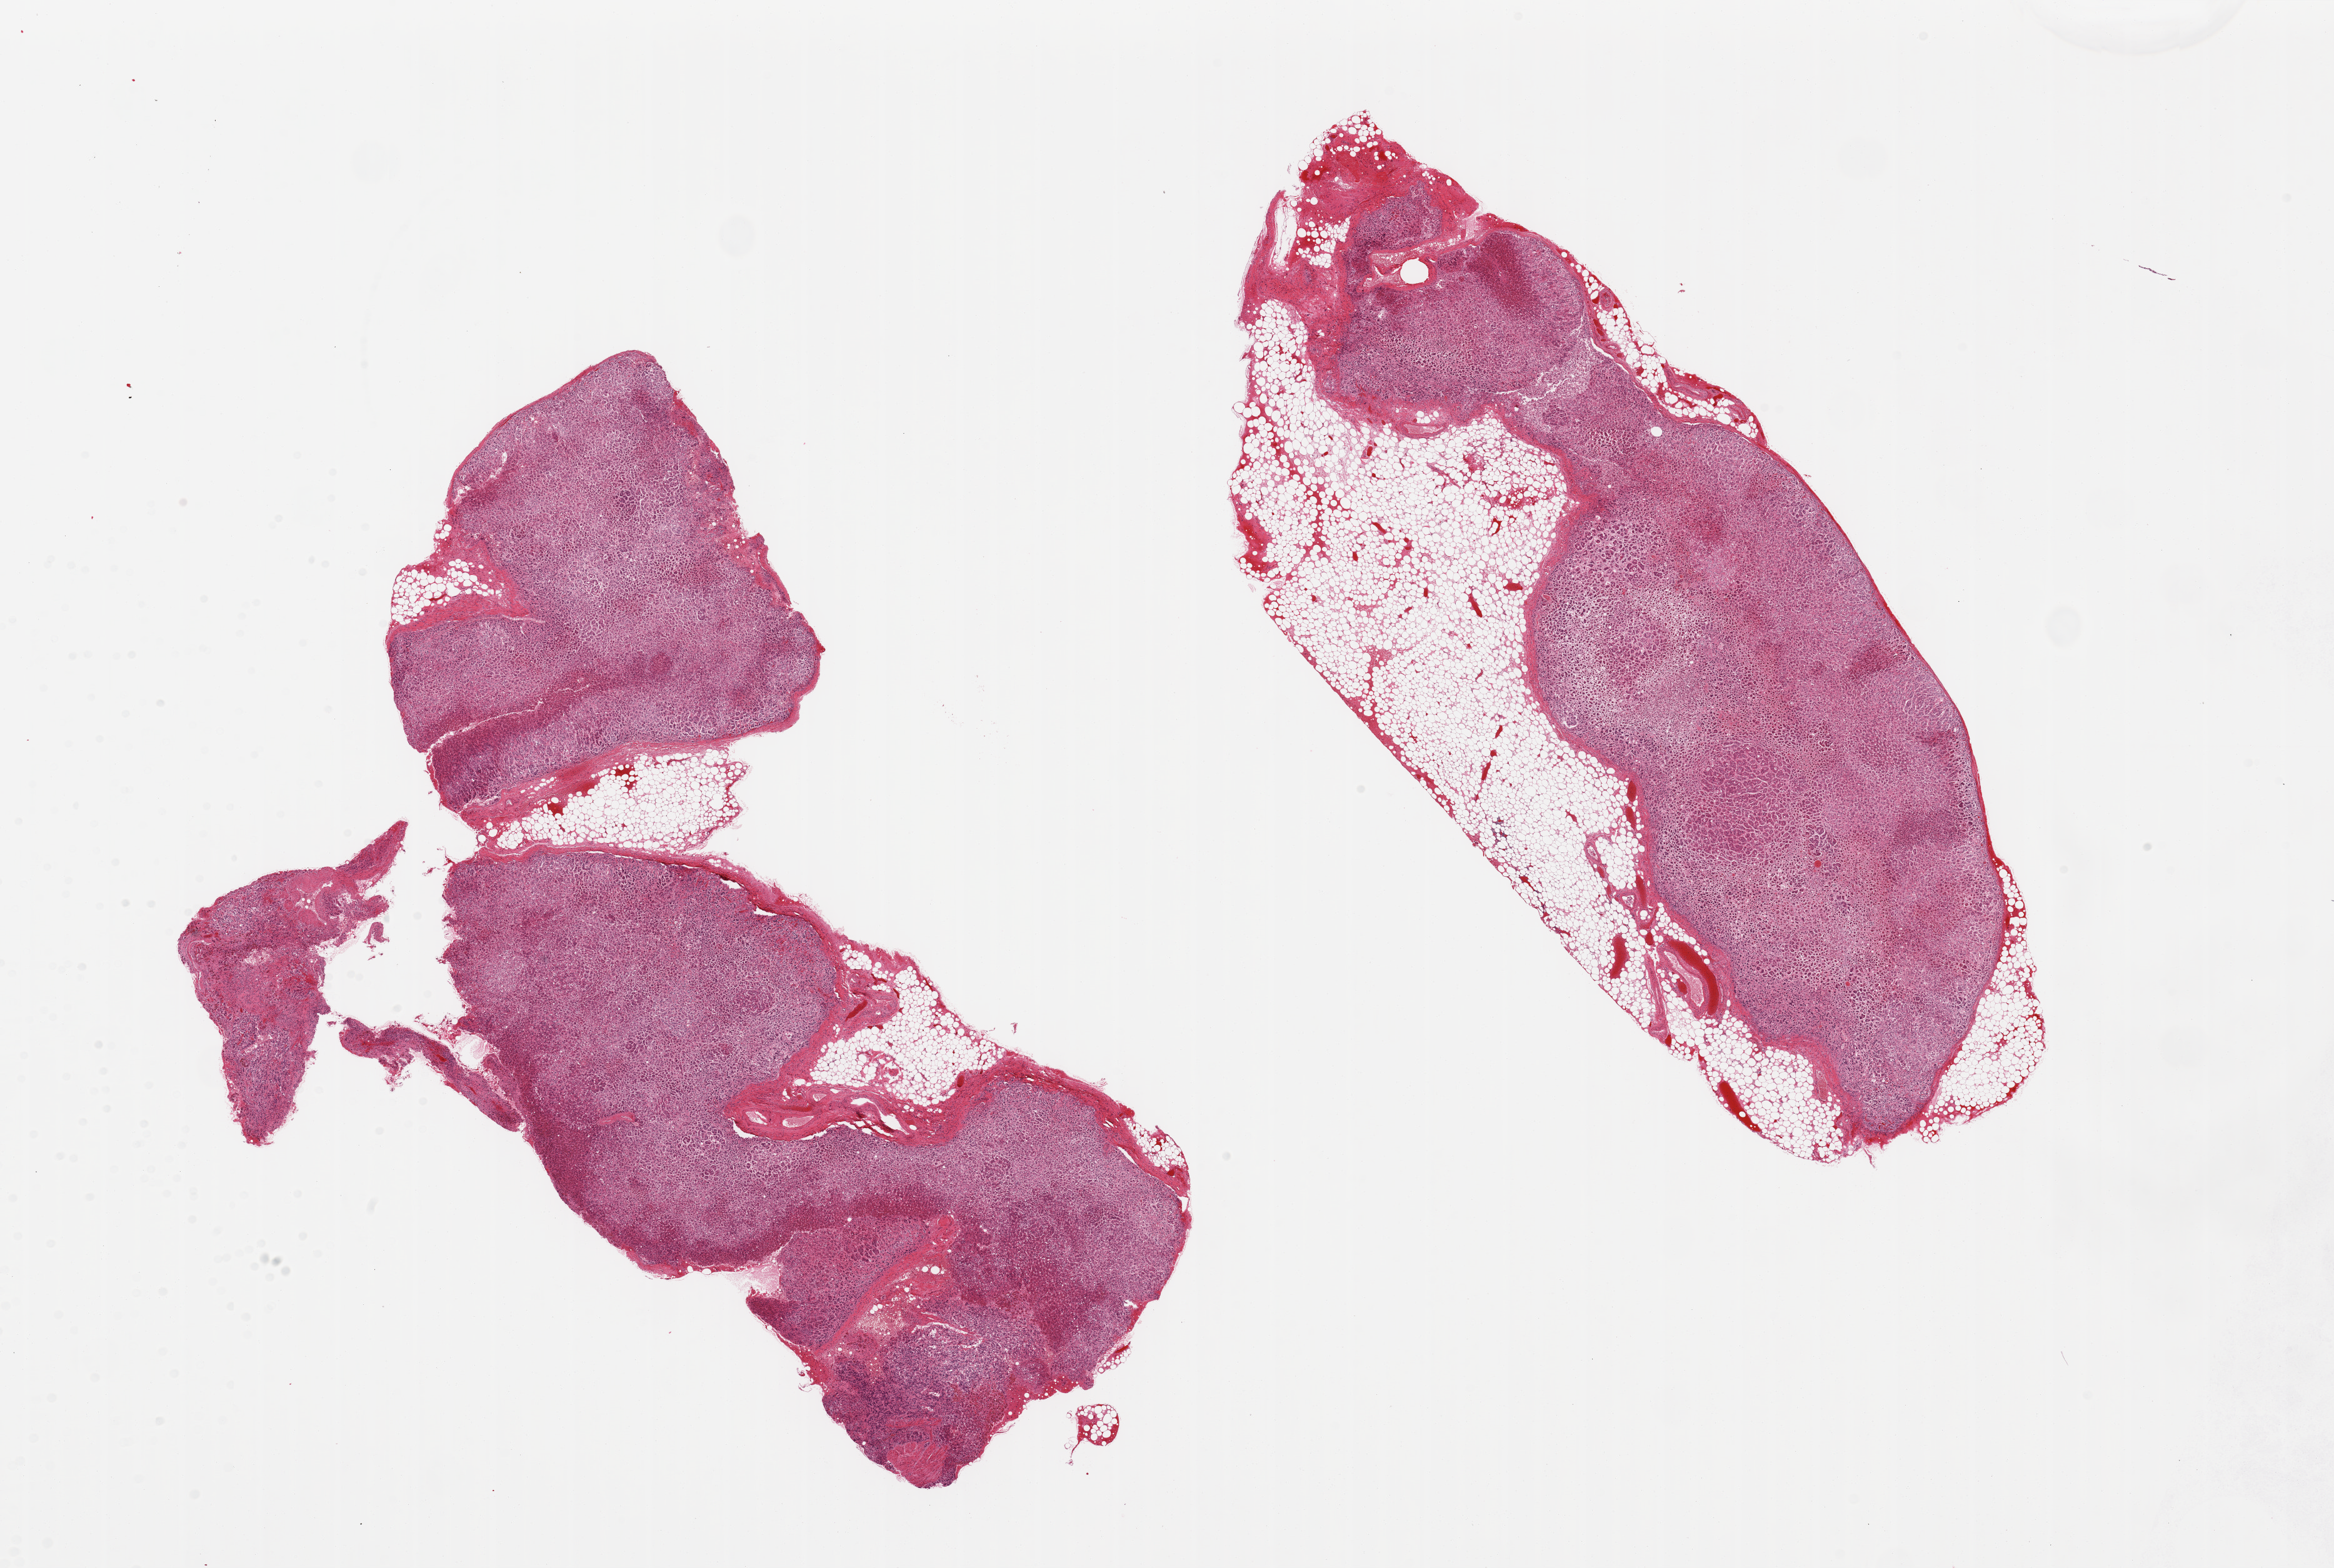
Whole-slide image, hematoxylin and eosin (H&E) stain, shown as a low-resolution overview of the whole scanned area (about 29.5 x 19.8 mm), PAXgene-fixed paraffin-embedded (PFPE) section, target tissue: adrenal gland, donor tissue sample.
* pathologist's review note for this sample: 3 pieces, ~40% adherent fat; All cortex only, advanced autolysis